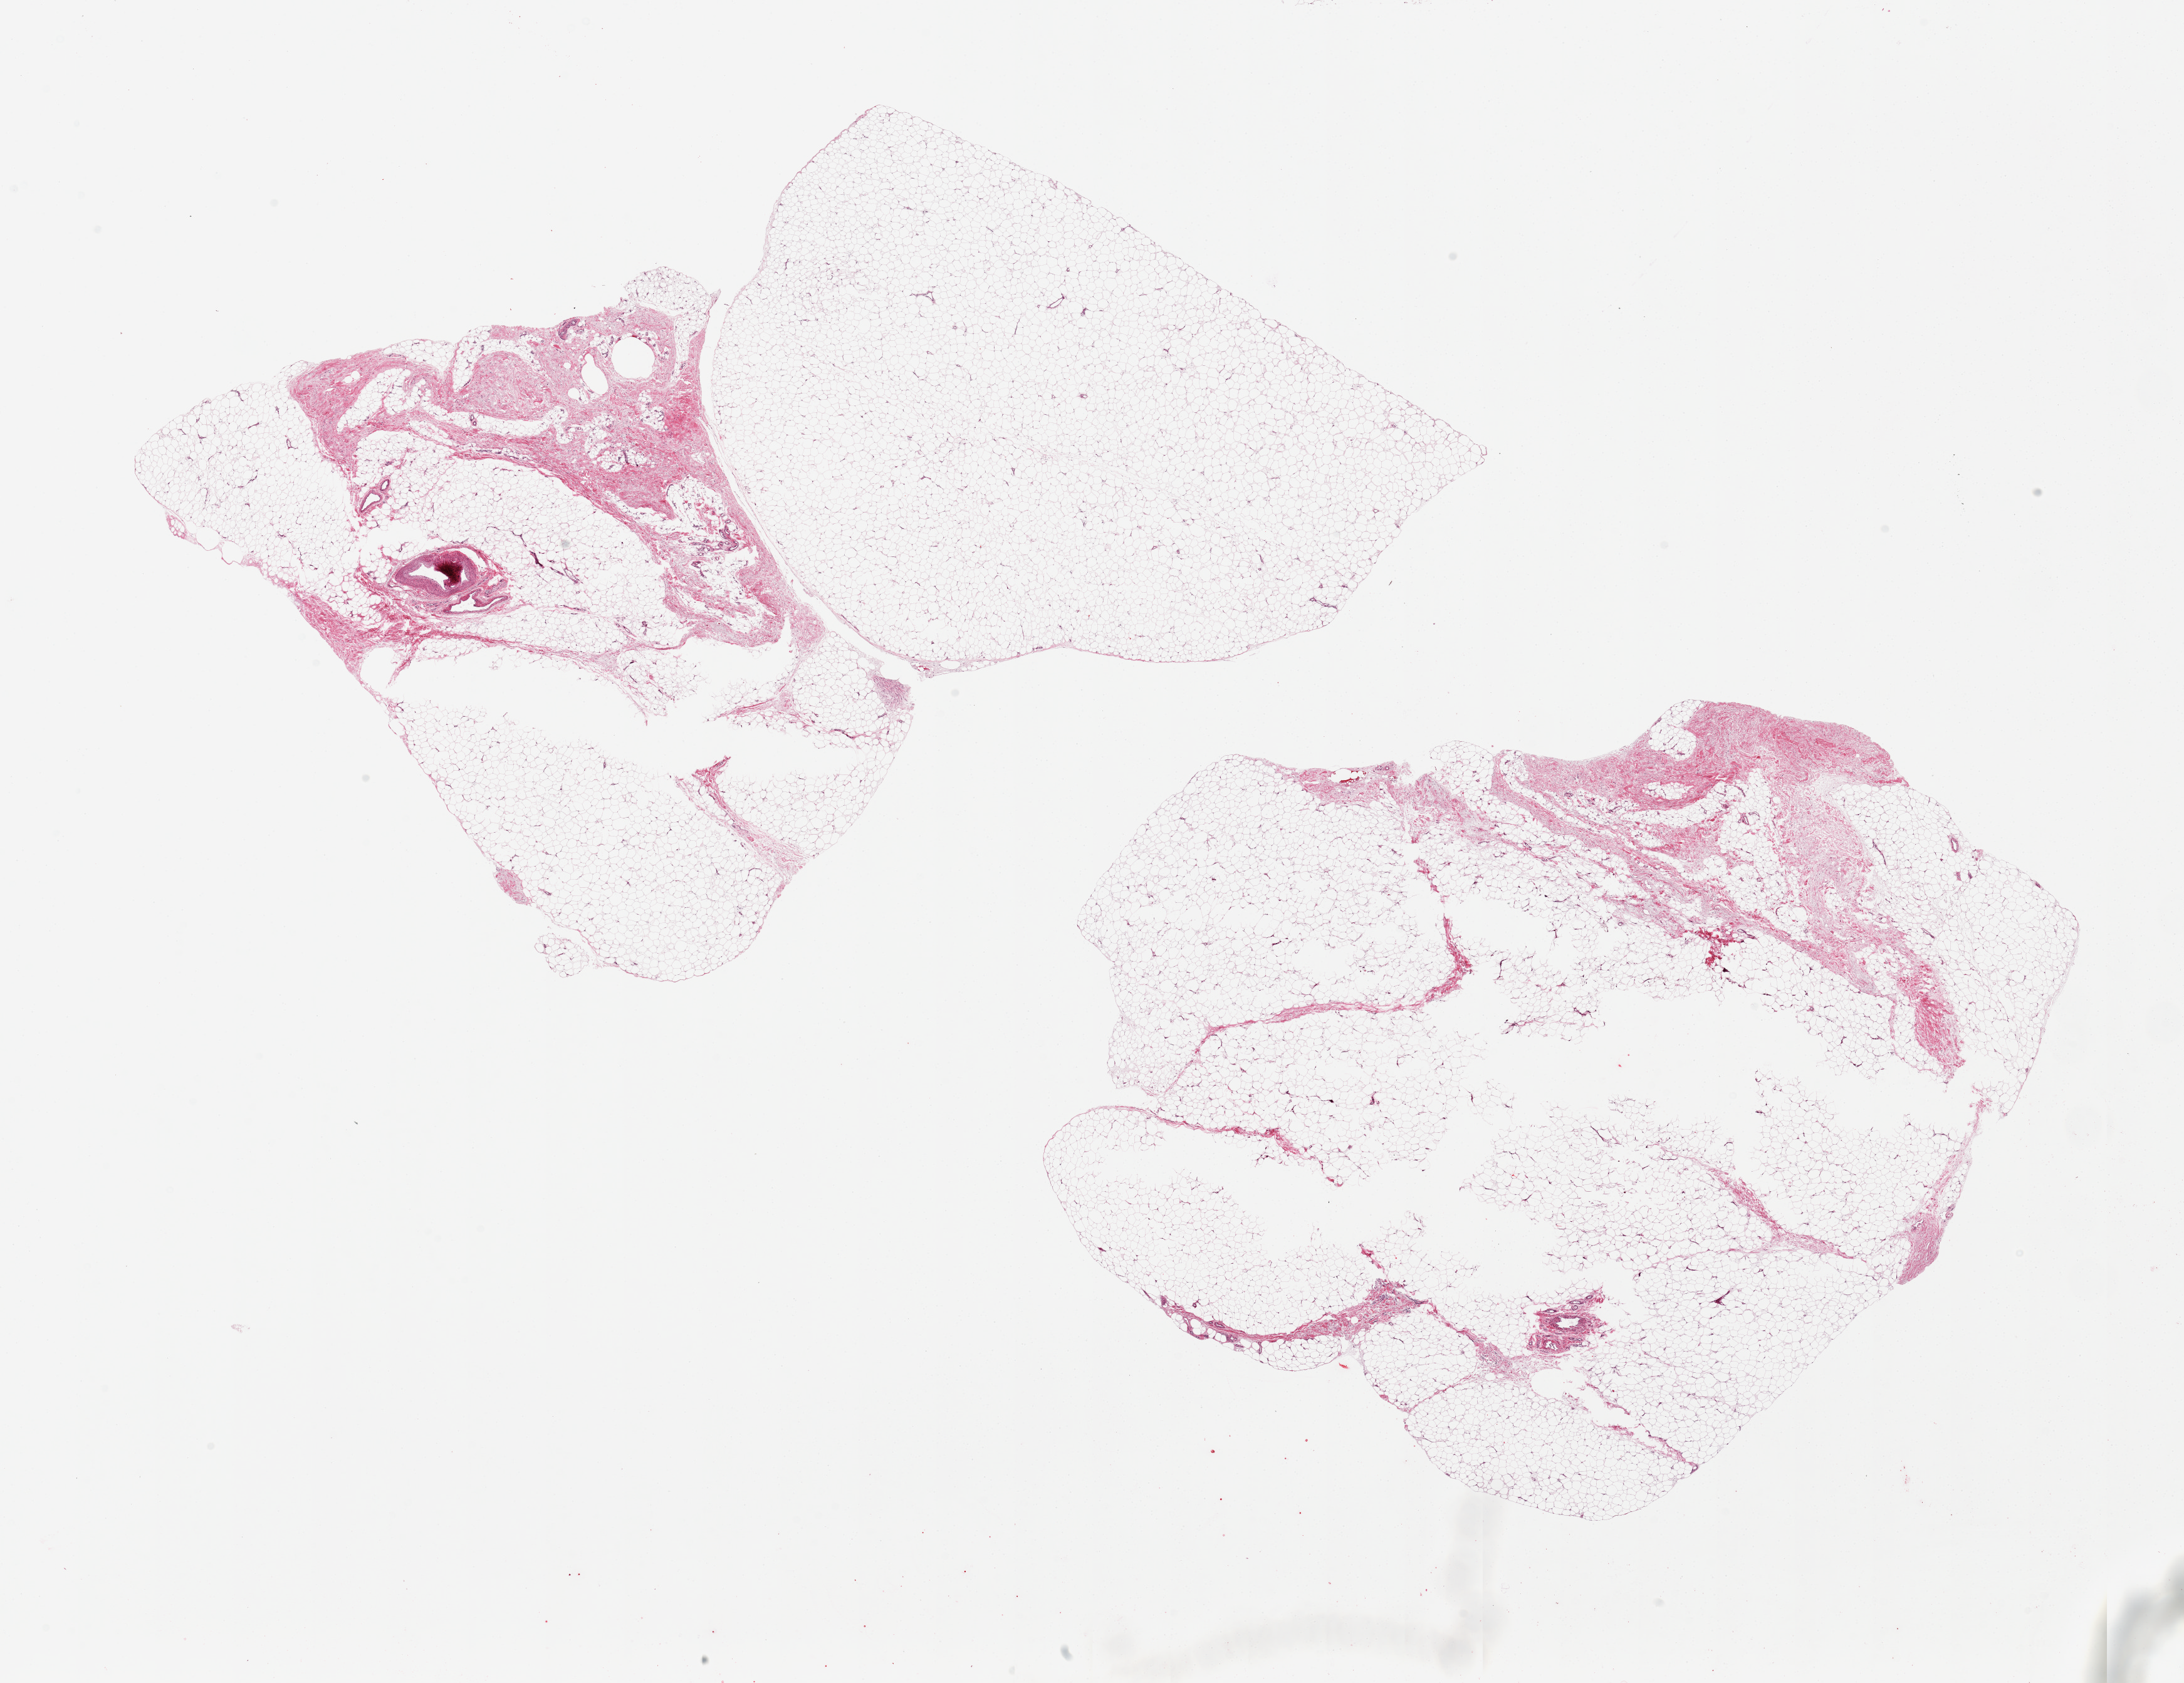
H&E whole-slide image, brightfield, a low-resolution overview of the entire scanned area, about 27.6 x 21.2 mm (slide scanned at 20x). PAXgene-fixed, paraffin-embedded tissue. Section of adipose tissue (target tissue). Donor tissue sample. Male donor.
Reviewer comment on this tissue sample: 2 pieces, each with ~10% fibrous stroma, one with a prominent vessel.